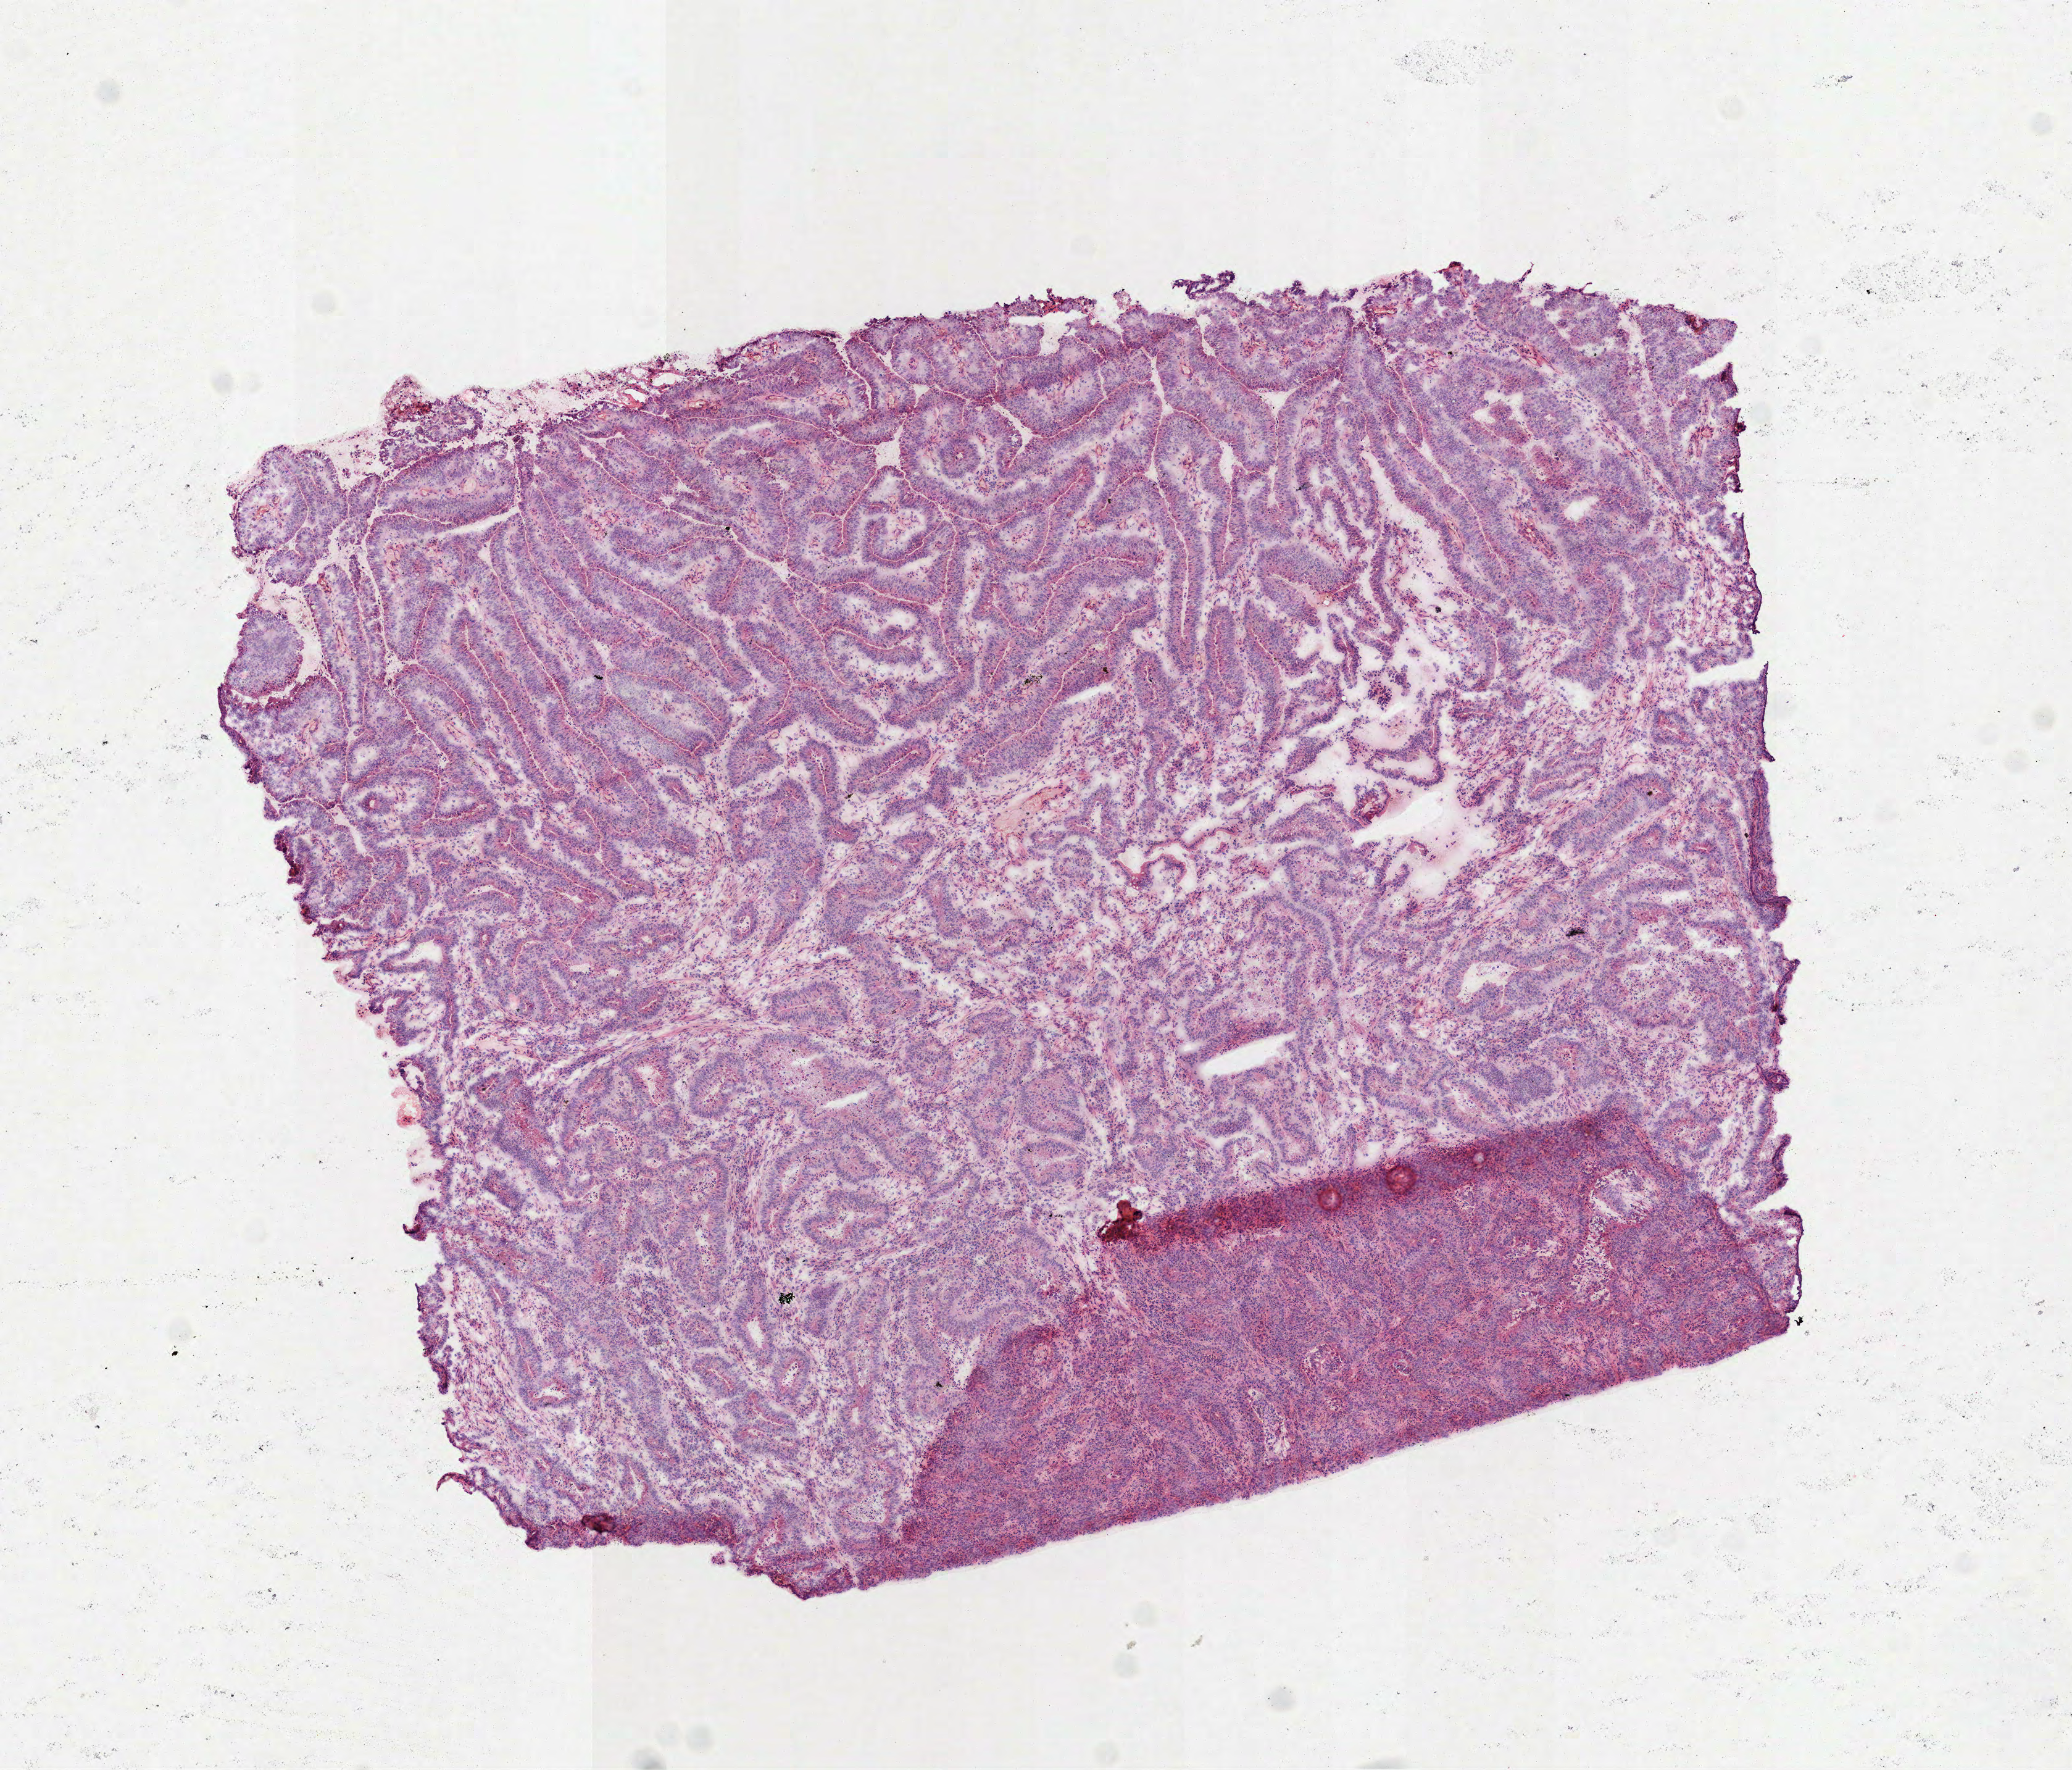
H&E-stained whole-slide image — whole scanned area (about 6.8 x 5.8 mm, slide scanned at 40x) shown as a low-resolution overview, frozen section, sample: primary tumour, colon. Male, age 53 years at initial diagnosis. Composition of this section per pathologist review: tumour cells 99%, tumour nuclei 80%.
Histologic diagnosis: Adenocarcinoma, NOS.